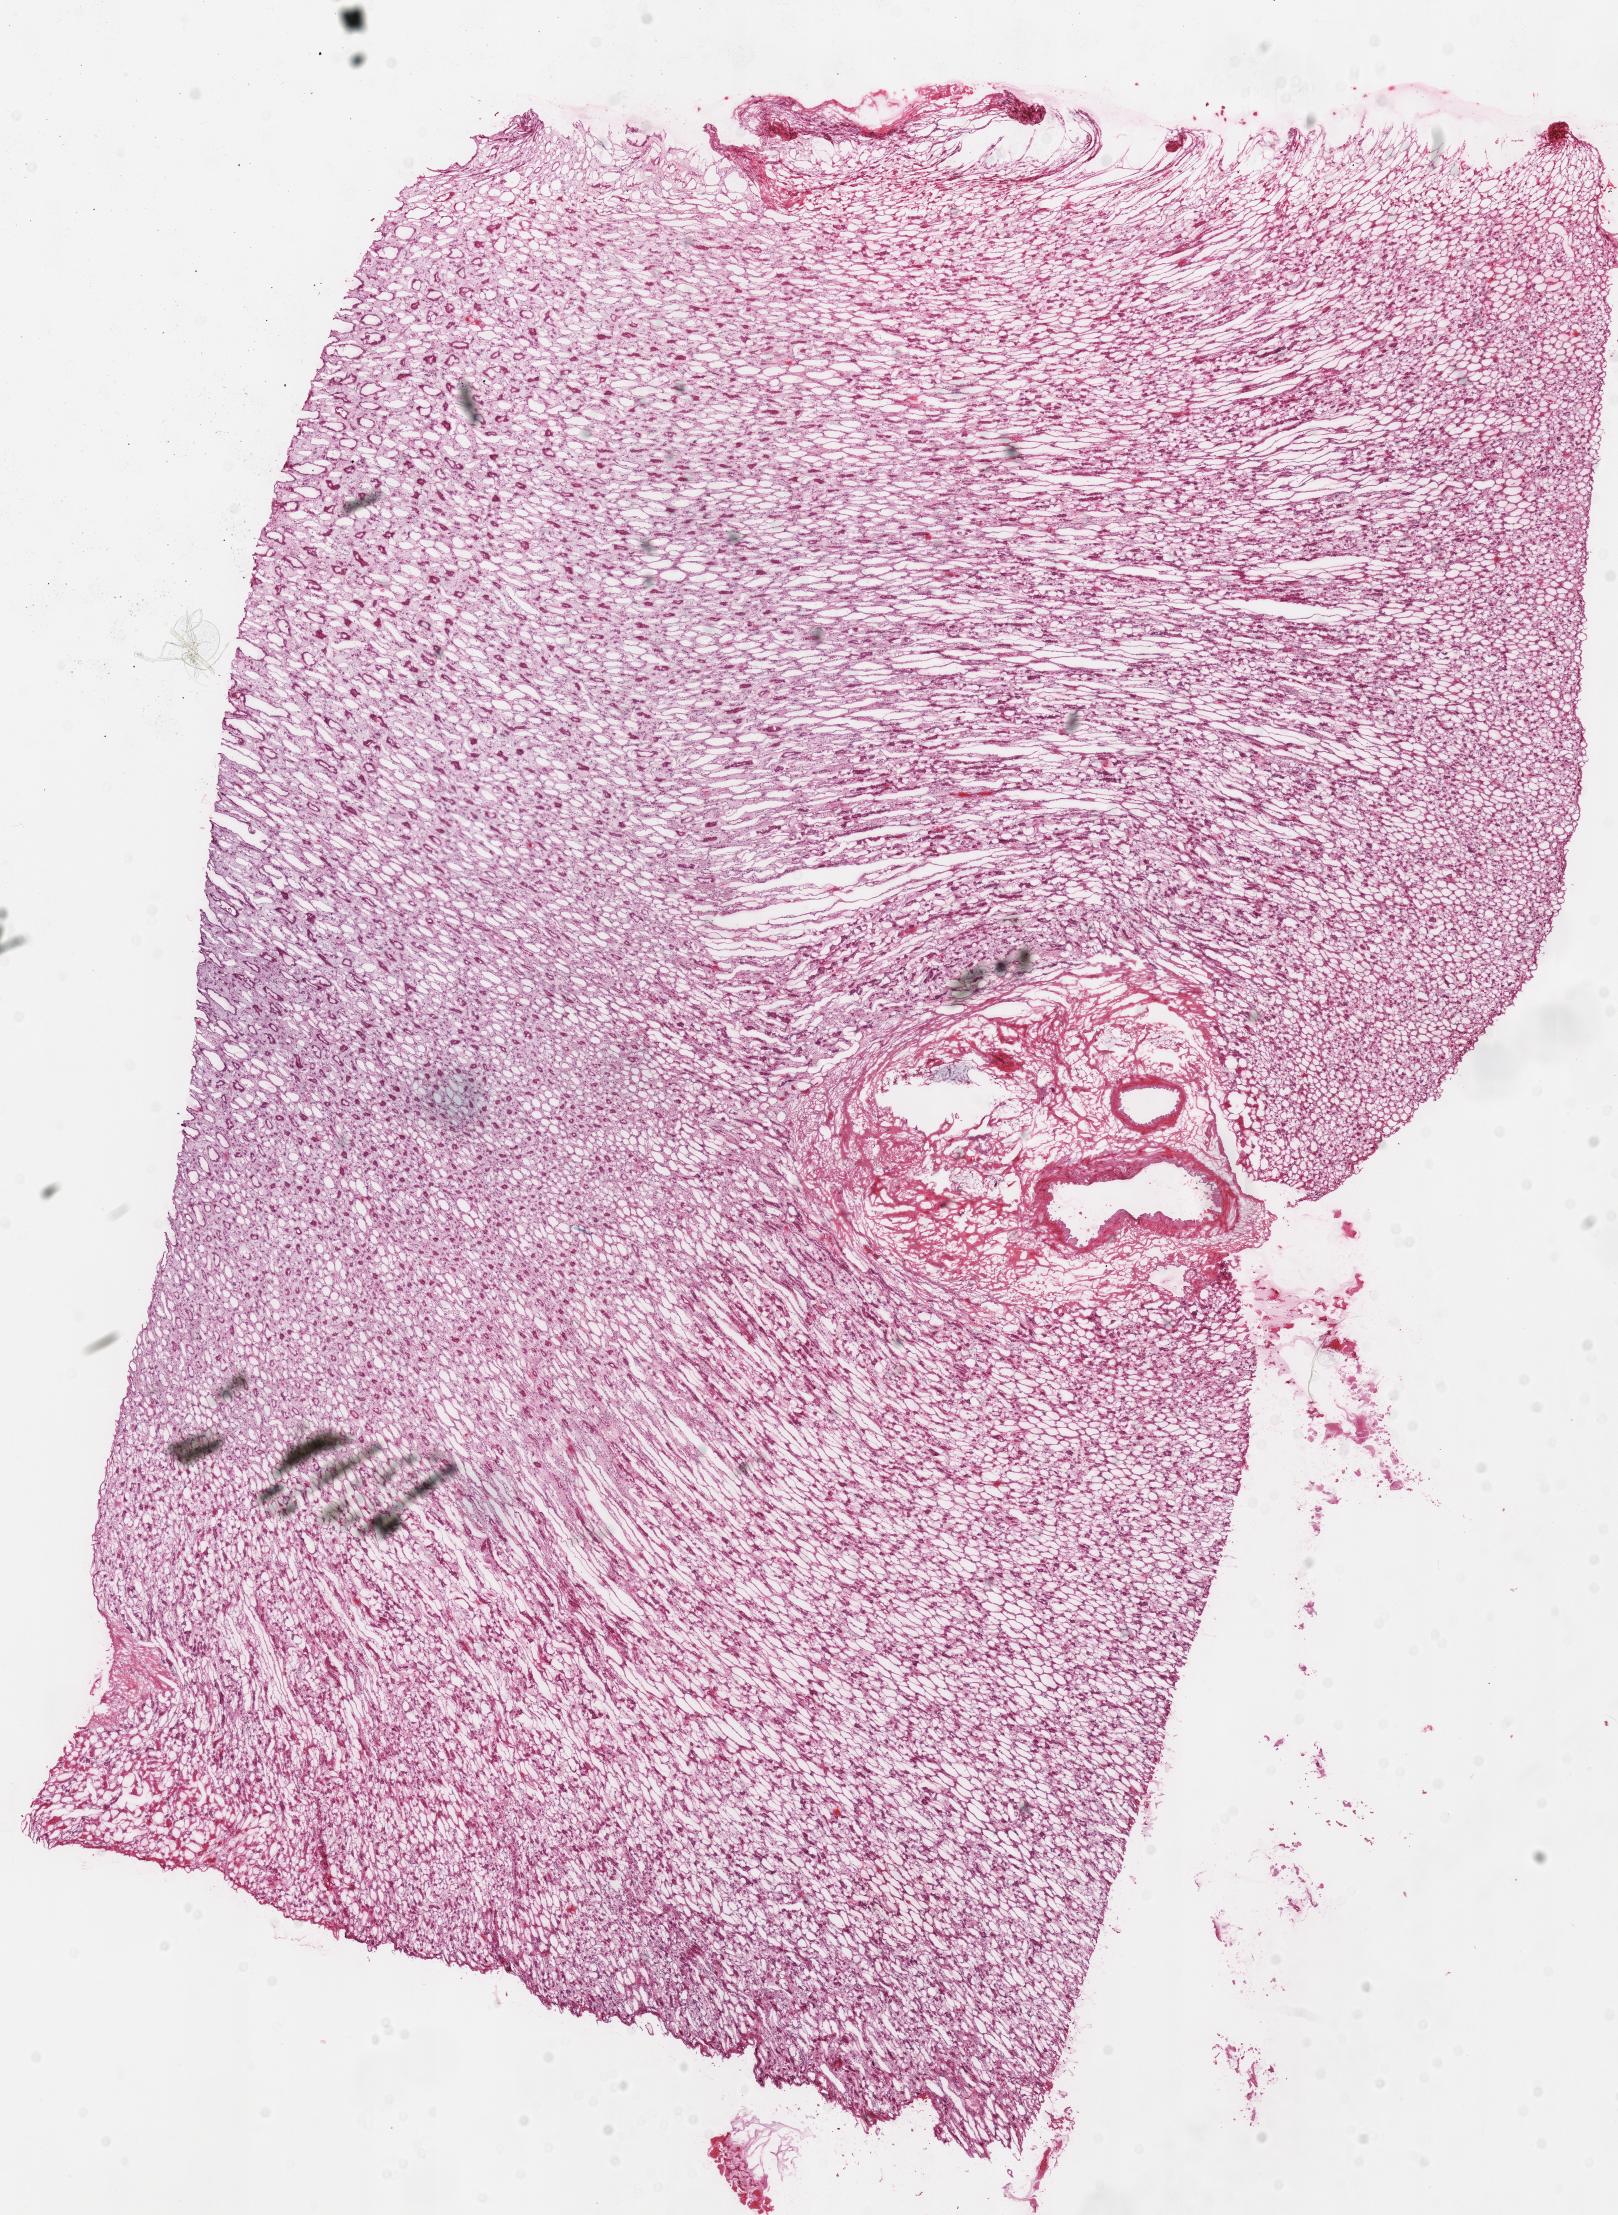
Hematoxylin and eosin (H&E) stained whole-slide image, shown as a low-resolution overview of the whole scanned area (about 12.7 x 17.4 mm). Frozen section from the top of the tissue portion. Kidney, solid tissue normal (non-tumour tissue) sample. Female patient; age at initial diagnosis 35 years. Infiltration values recorded for this section: lymphocyte infiltration 0%, monocyte infiltration 0%, neutrophil infiltration 0%.
This section: solid tissue normal (non-tumour) sample from the same patient. Patient diagnosis: Renal cell carcinoma, chromophobe type.